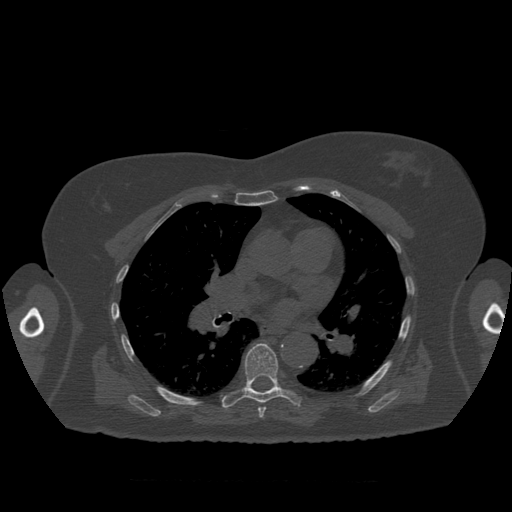
CT including the spine, one axial slice. Position 398 of 399 along the scan axis. 120 kVp. Bone window (W 1800 / L 400 HU). 1.25 mm slice thickness. 512 × 512 image matrix, field of view 404 × 404 mm. Patient age 81 years. Case-level facts recorded for this patient, not image findings: primary cancer: renal; vertebrae with lytic lesions (as recorded): L1.
Outlined on this slice (semi-automatically segmented with operator editing):
- T7 vertebra: bounding box (x1, y1, x2, y2) in pixels: (221, 343, 301, 418)